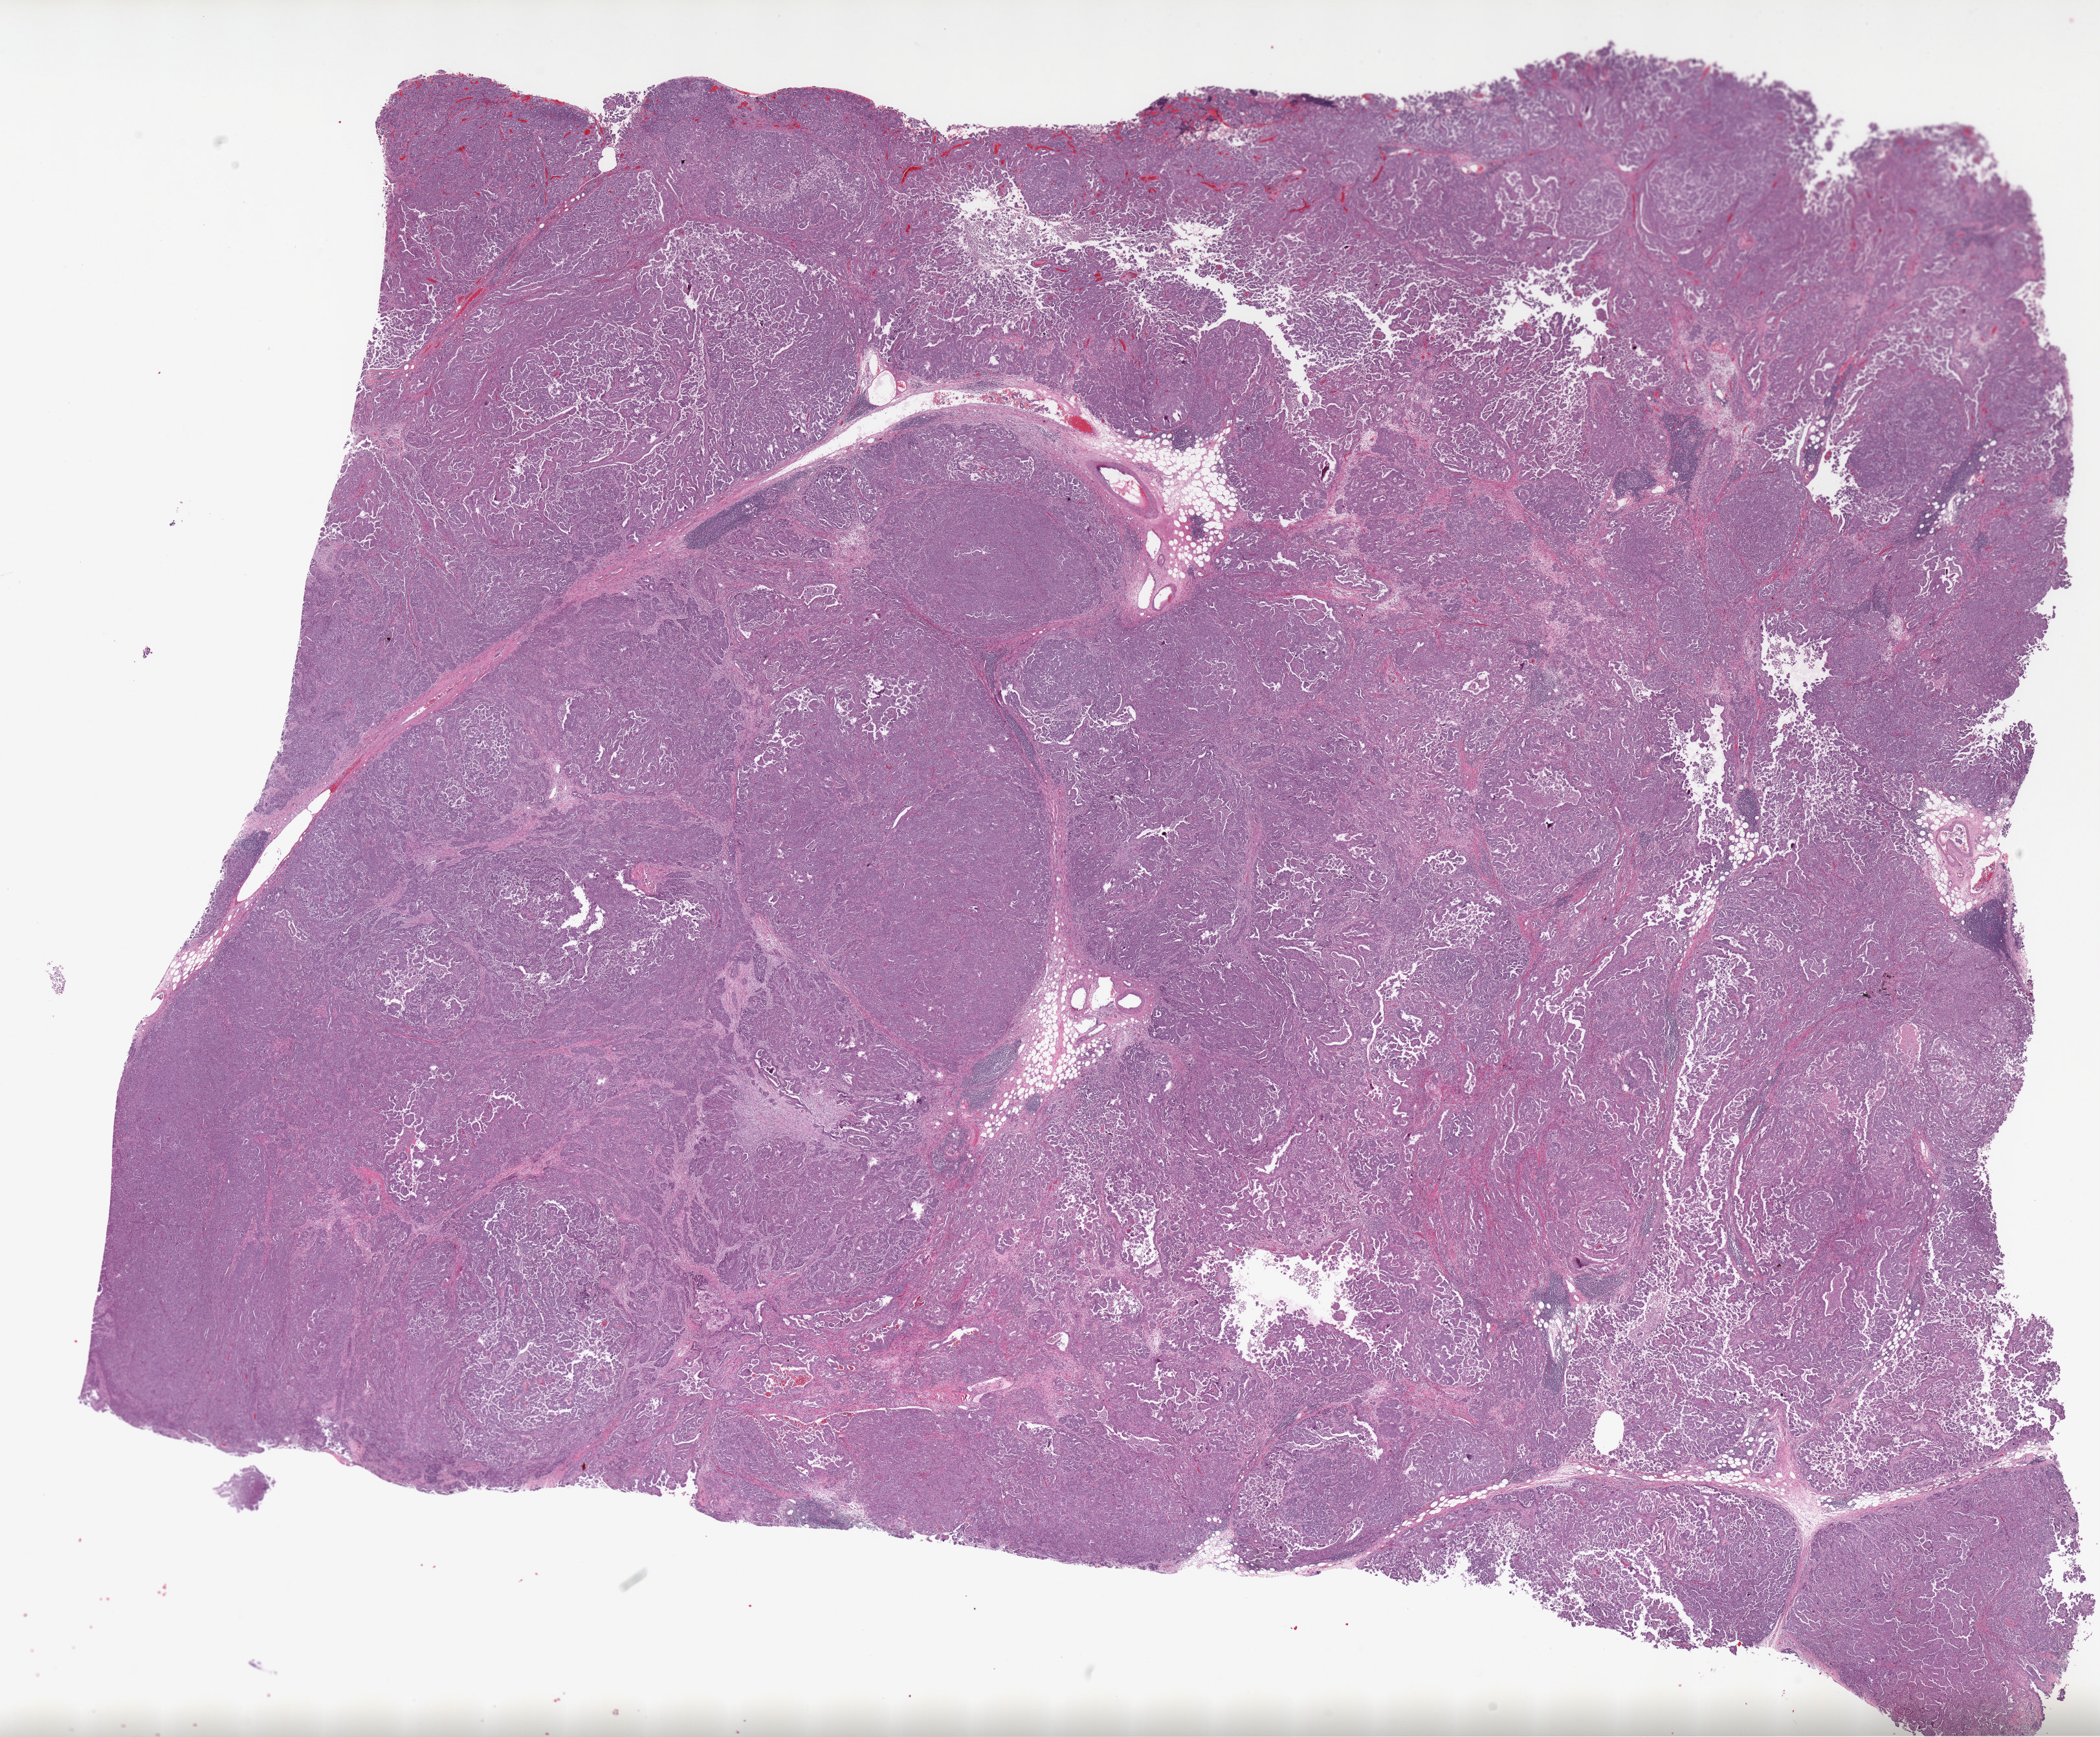
H&E-stained whole-slide image — whole scanned area (about 25.9 x 21.4 mm, acquisition: 20x scan) shown as a low-resolution overview. FFPE section. Ovary, primary tumour sample. Female patient; age at initial diagnosis 60 years. Histologic grade: G3 (poorly differentiated).
Diagnosis: Serous cystadenocarcinoma, NOS. FIGO stage: IV.